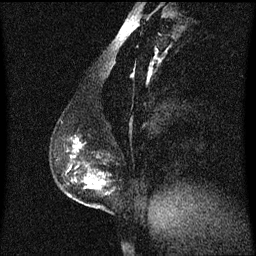
Breast MRI (dynamic contrast-enhanced), one sagittal slice; slice 25 of 60 in the series (ordered by position); dynamic contrast-enhanced series, image 2 of 3 at this slice position (ordered by acquisition); 1.5 T; TE 4.2 ms, TR 8.4 ms; 2 mm slice thickness; 256 × 256 image matrix, field of view 200 × 200 mm. Female patient, age 40 years. Case-level facts recorded for this patient, not image findings: setting: breast cancer imaged before/during neoadjuvant chemotherapy; receptor status: triple-negative.
Outlined on this slice (semi-automatic segmentation, software-assisted and operator-edited):
- analysis volume of interest (the breast-tissue region the enhancement analysis was run in; not a lesion): bounding box [x1, y1, x2, y2] px = [60, 138, 109, 209]
- tumour enhancement mask (voxels above the 70 % enhancement threshold inside the analysis volume of interest): [74, 140, 103, 185]